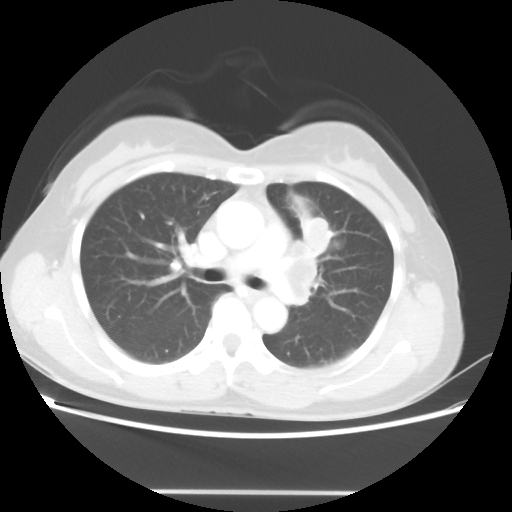
Chest CT, one axial slice; position 28 of 46 along the scan axis; reconstruction kernel STANDARD; lung window (W 1500 / L -600 HU); 512 × 512 image matrix. Female patient, age 50 years. From the clinical record (not read from this slice): clinical TNM (as recorded): T1c N1 M0.
Structures marked on this image (rectangle marked by the reading radiologist):
- lung tumour (recorded histology: adenocarcinoma): box from (x=300, y=214) to (x=334, y=253) px